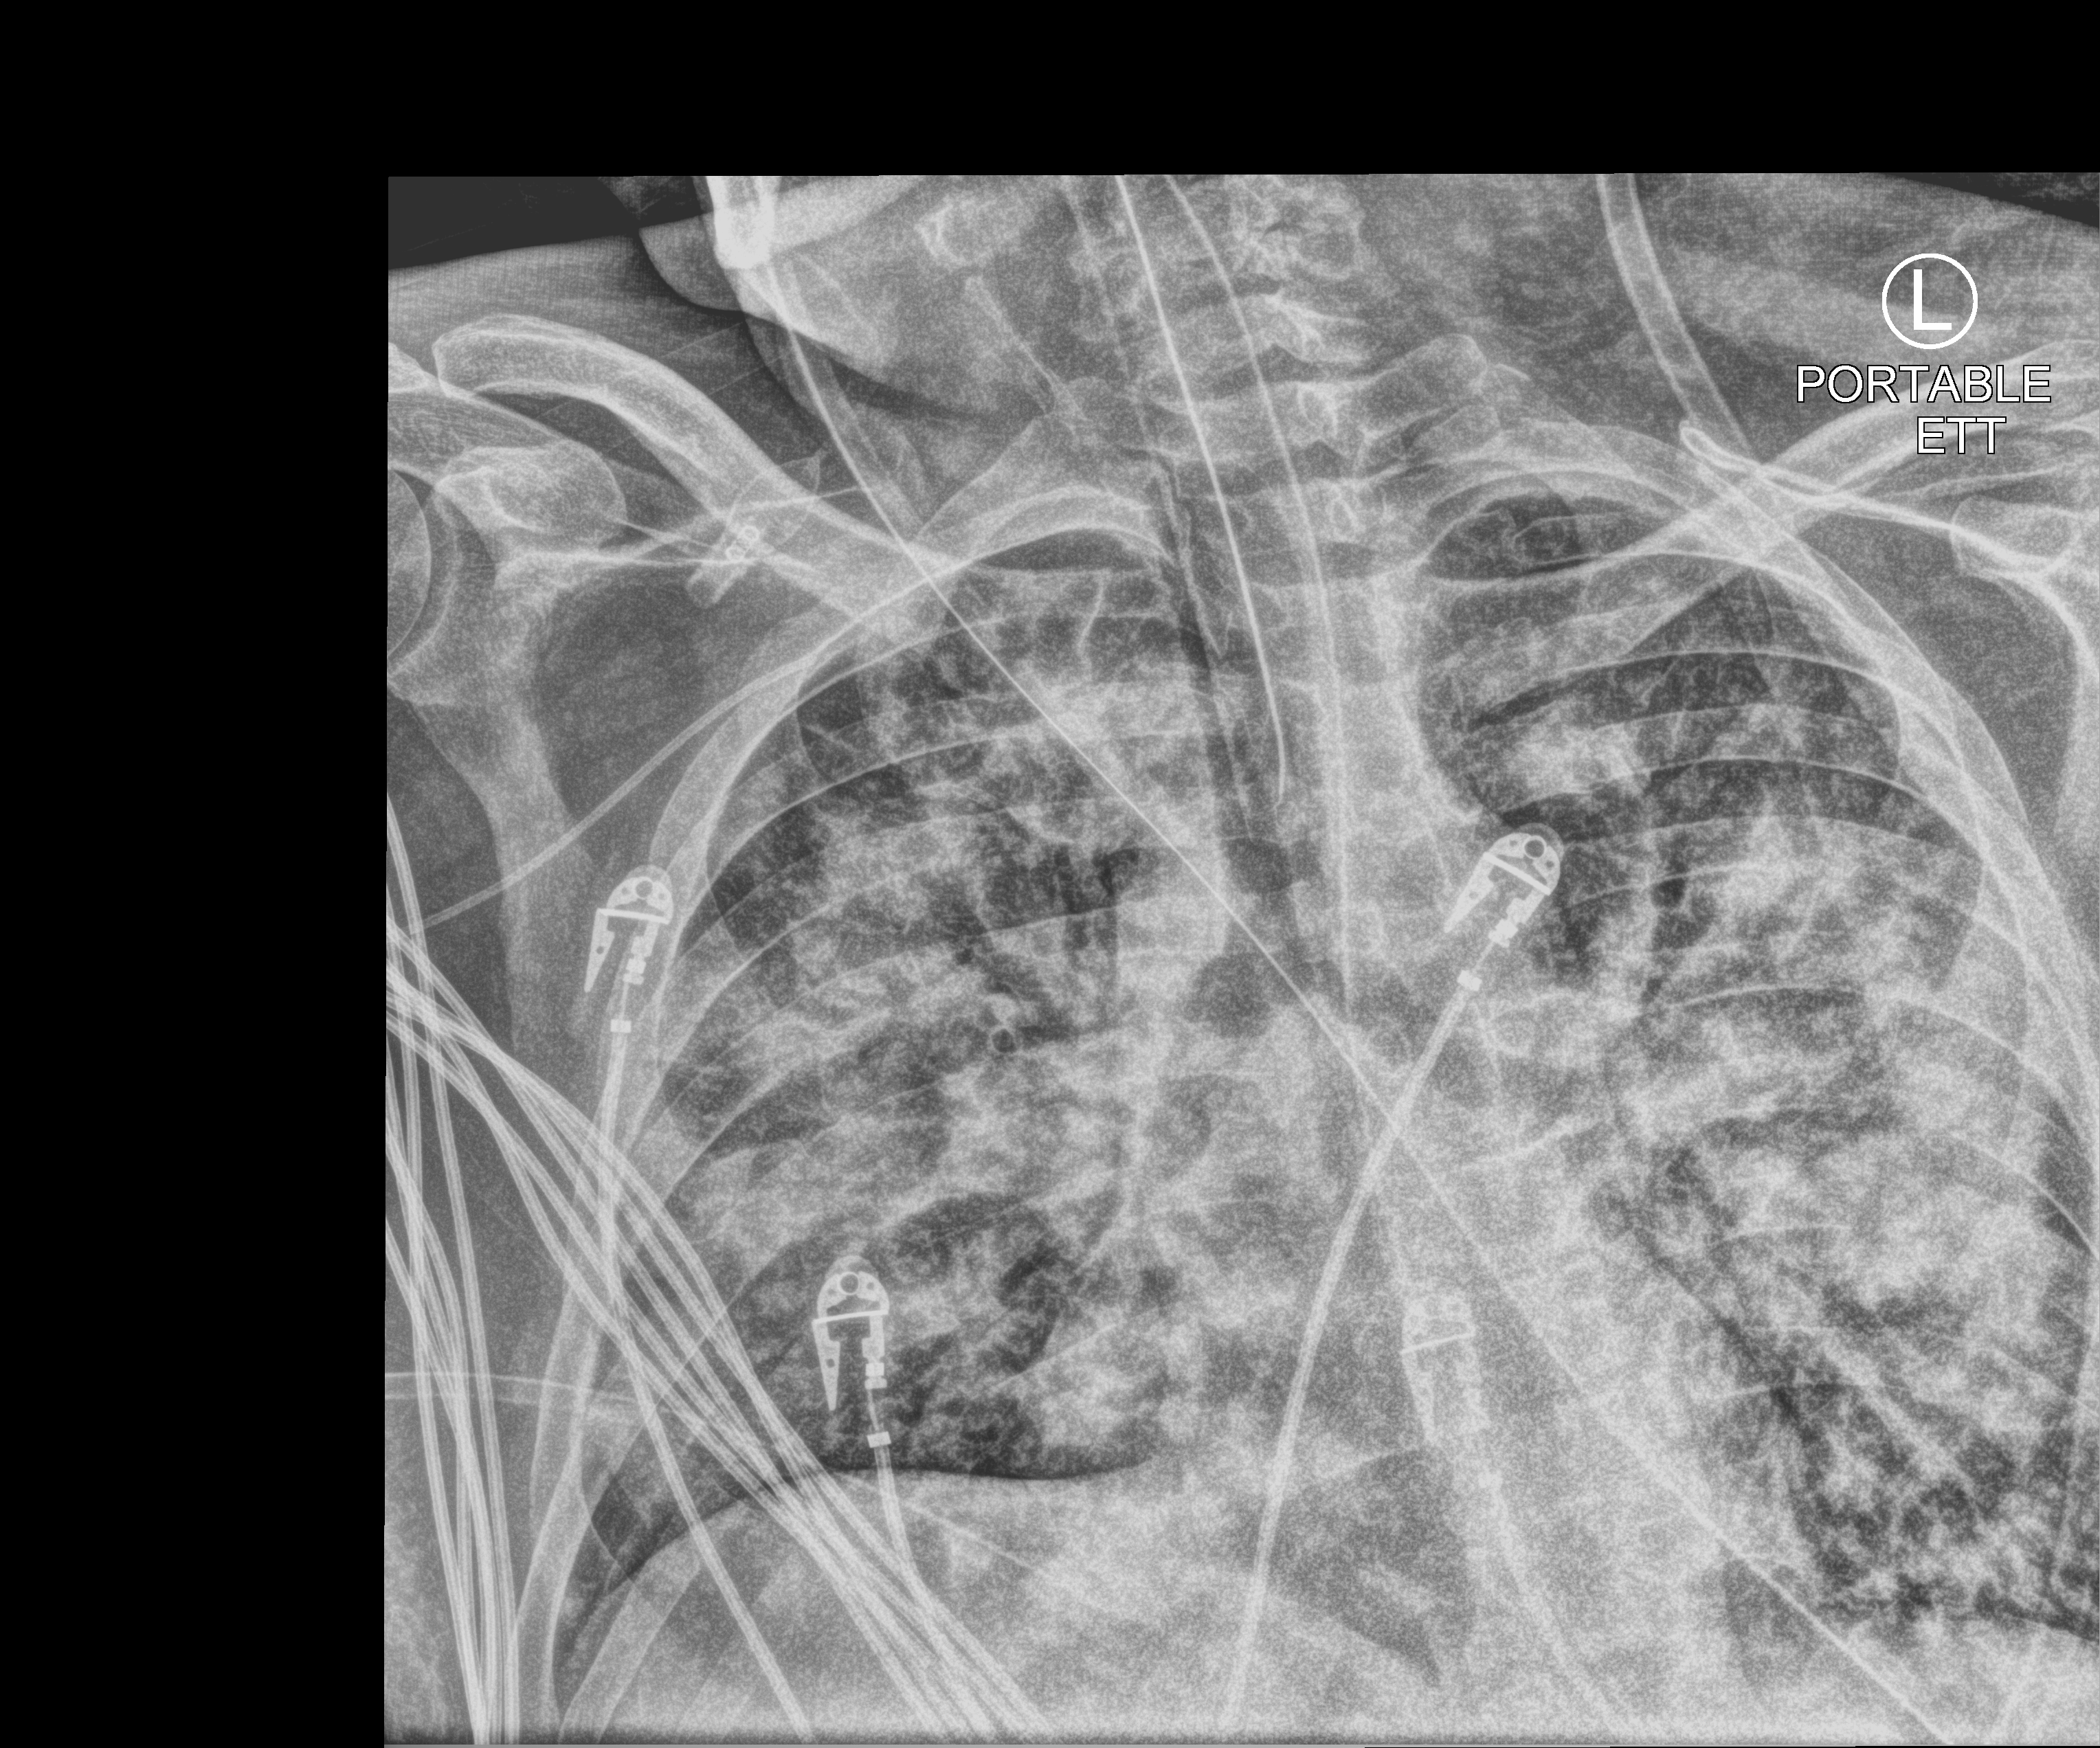
Bedside chest radiograph (computed radiography); anteroposterior (AP) projection. Male patient hospitalised with COVID-19, age 18–59 years.
Hospital-stay facts (about this admission, not read from this image; timing relative to this image not recorded): COPD (admission record): no.